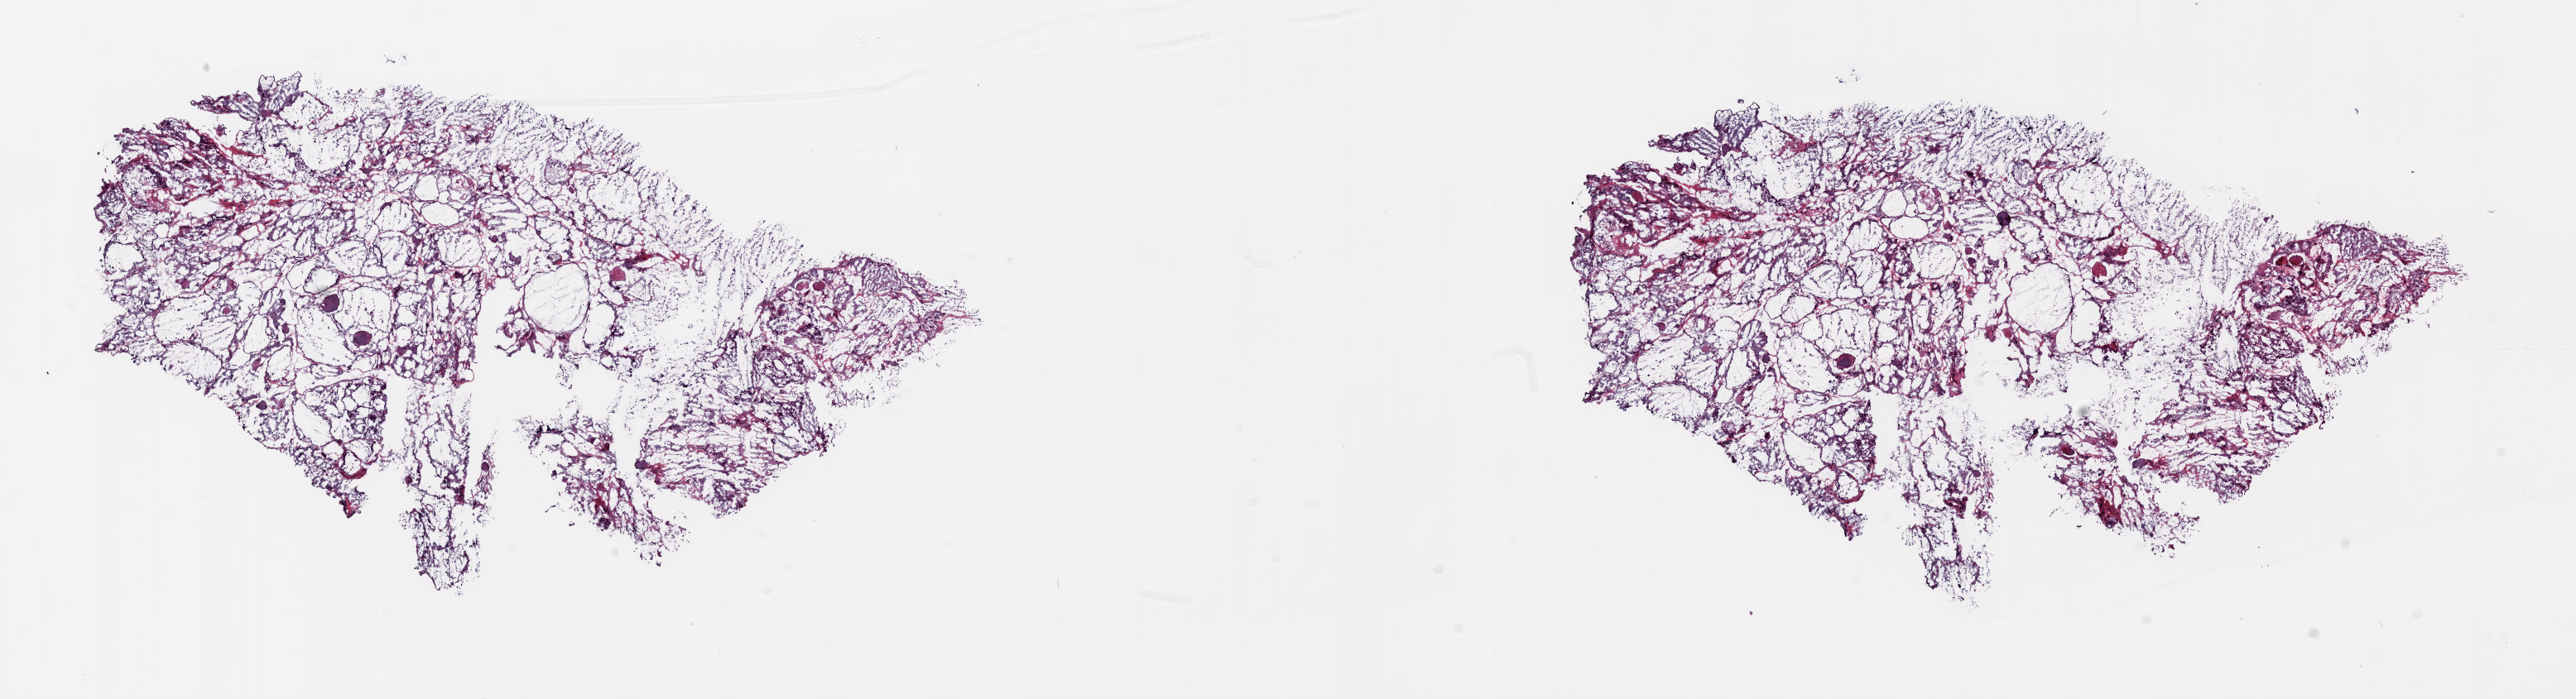
H&E whole-slide image, shown as a low-resolution overview of the whole scanned area (about 24.6 x 6.7 mm); frozen section from the top of the tissue portion; solid tissue normal (non-tumour tissue) sample from the thyroid. Male, age 66 years at initial diagnosis. Composition of this section per pathologist review: tumour cells 0%, tumour nuclei 0%, normal cells 100%, stromal cells 0%, necrosis 0%. Infiltration values recorded for this section: lymphocyte infiltration 0%, monocyte infiltration 2%, neutrophil infiltration 0%.
* this section: solid tissue normal sample (biorepository sample class)
* patient diagnosis: Papillary adenocarcinoma, NOS (thyroid gland)